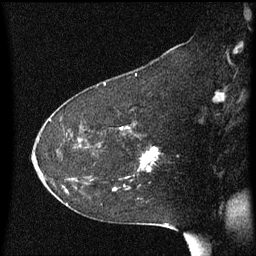
Breast MRI (dynamic contrast-enhanced), one sagittal slice; position 36 of 60 along the scan axis; dynamic contrast-enhanced series, image 2 of 3 at this slice position (ordered by acquisition); 1.5 T; TE 4.2 ms, TR 8.4 ms; 2 mm slice thickness; 256 × 256 image matrix. Patient: female, 54 years. From the clinical record (not read from this slice): setting: breast cancer imaged before/during neoadjuvant chemotherapy; receptor status: HR-positive, HER2-negative.
Annotated regions visible in this slice (semi-automatically segmented with operator editing):
- analysis volume of interest (the breast-tissue region the enhancement analysis was run in; not a lesion): bounding box [x1, y1, x2, y2] px = [120, 132, 161, 181]
- tumour enhancement mask (voxels above the 70 % enhancement threshold inside the analysis volume of interest): [139, 148, 157, 171]